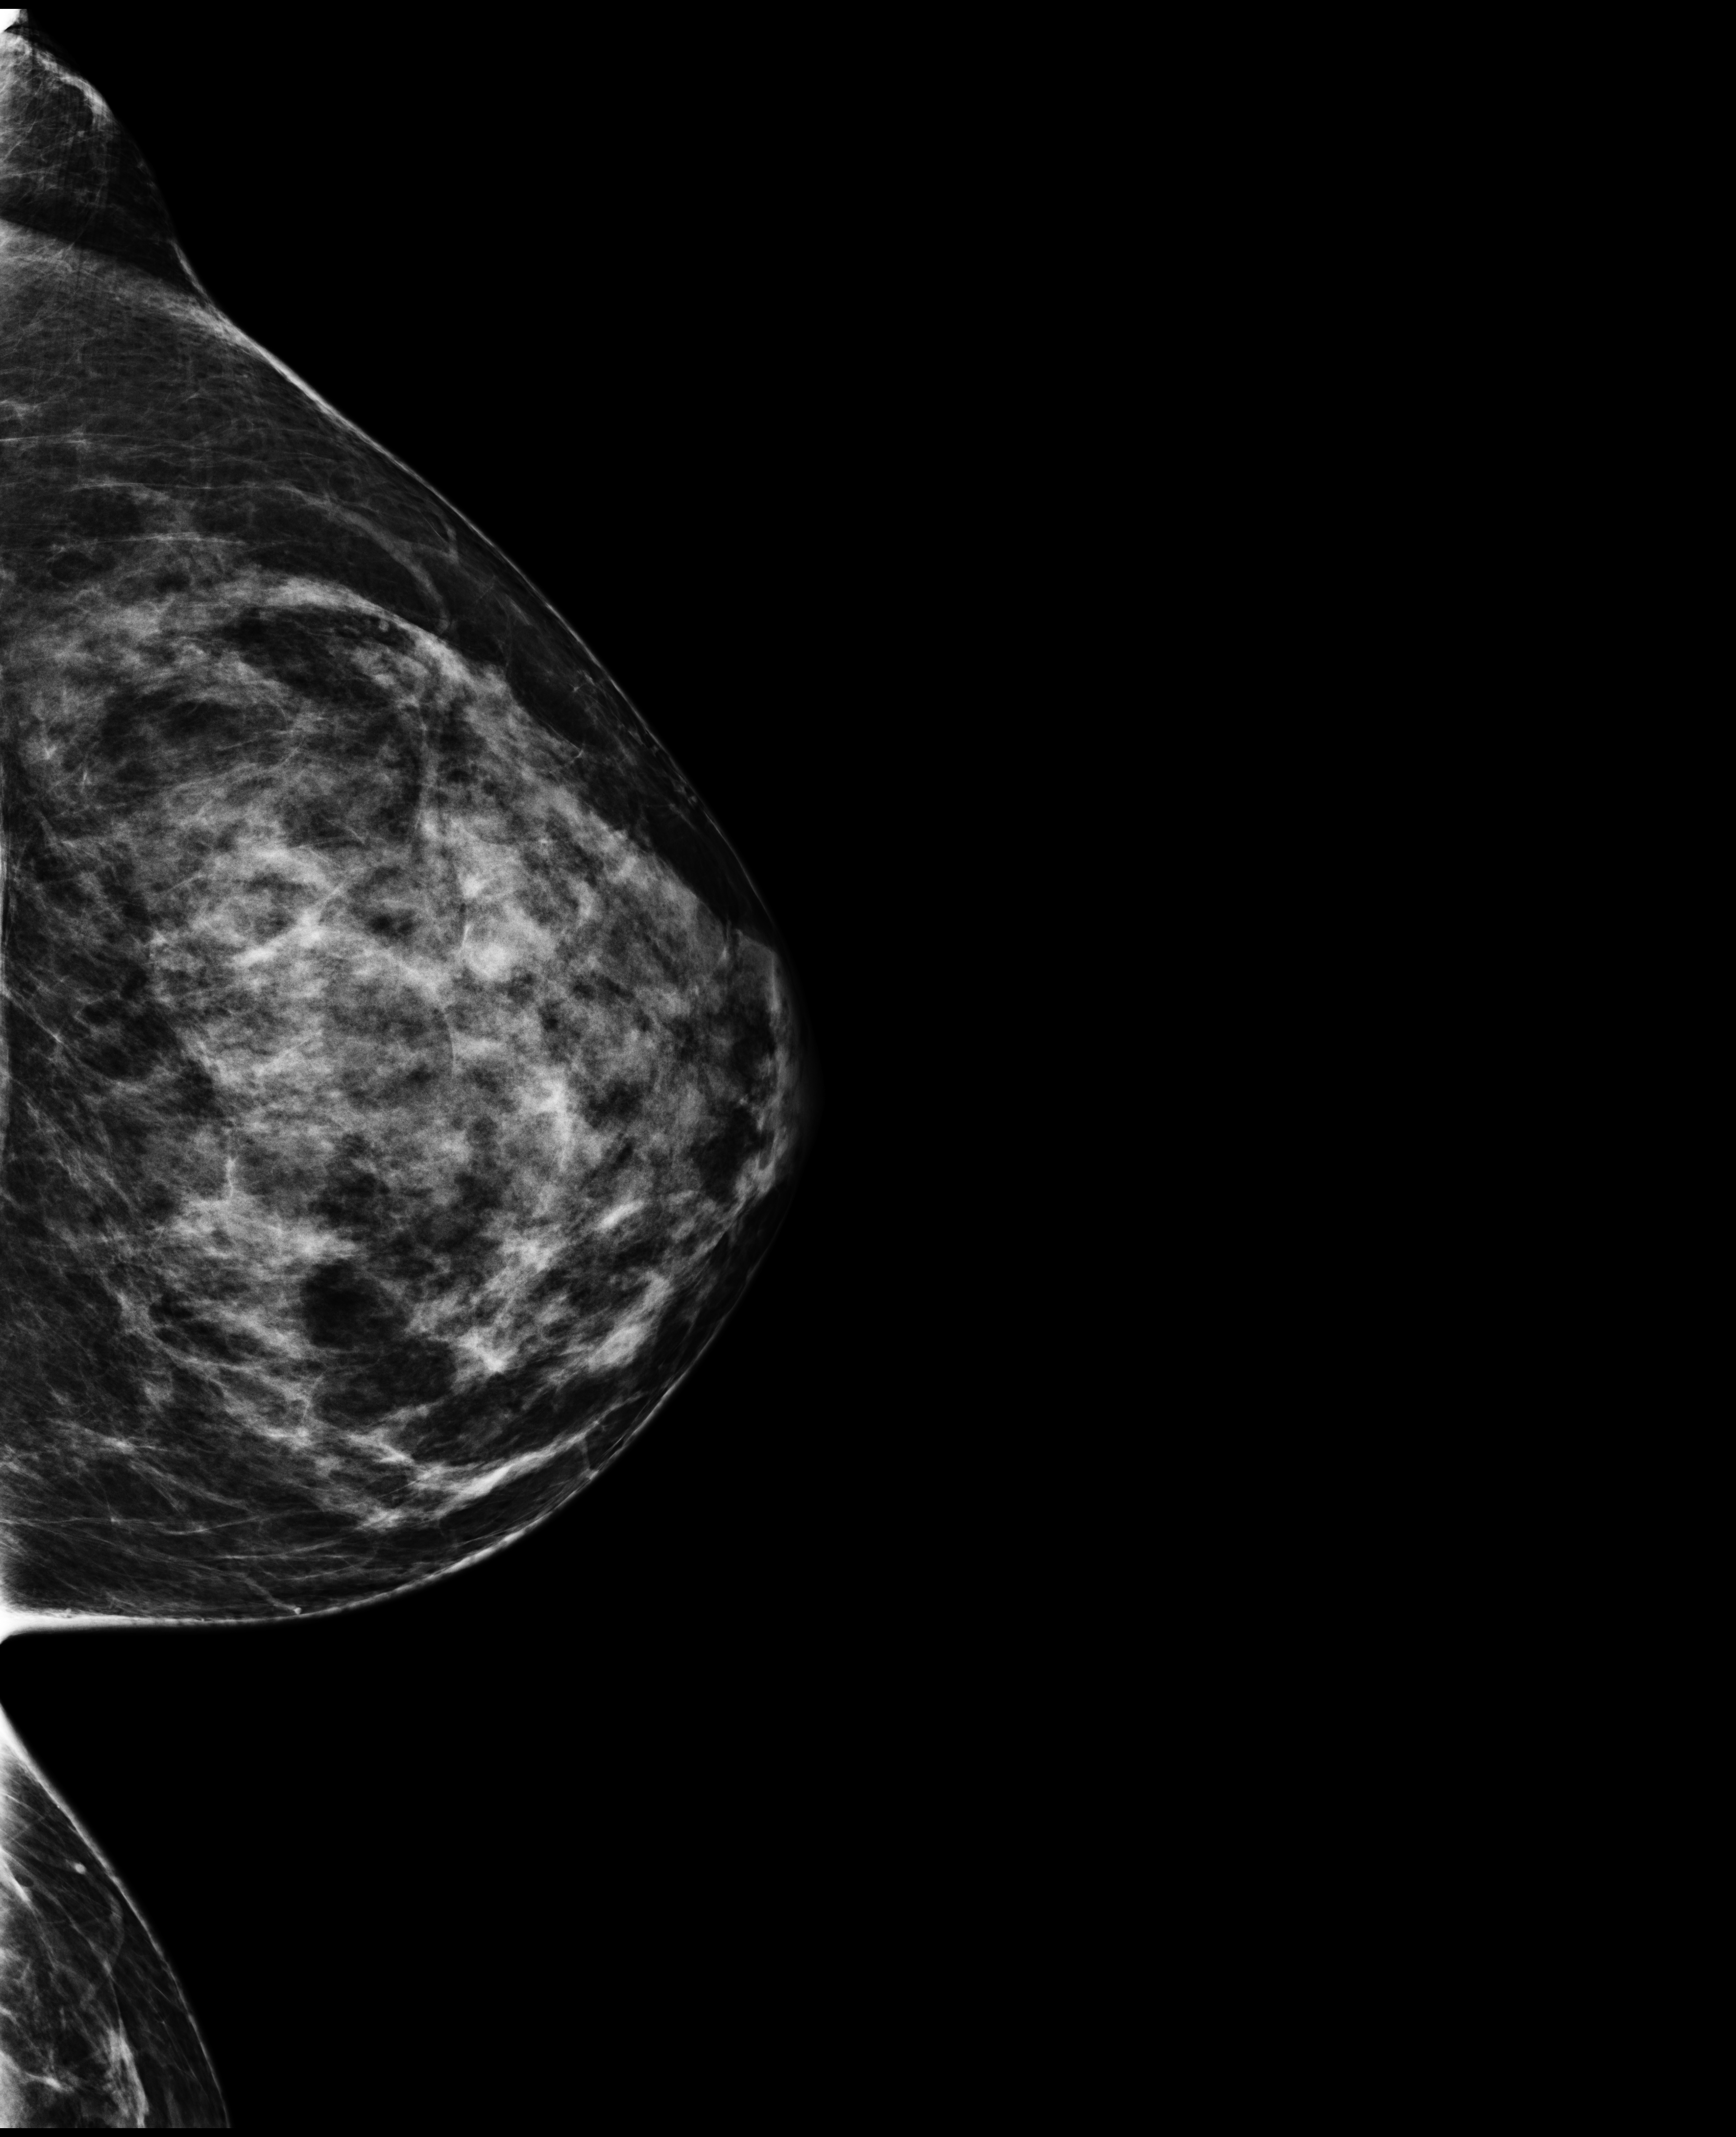
Screening examination. Female patient, age 43 years.
Image type: full-field digital mammogram. Breast: left. Projection: CC view.